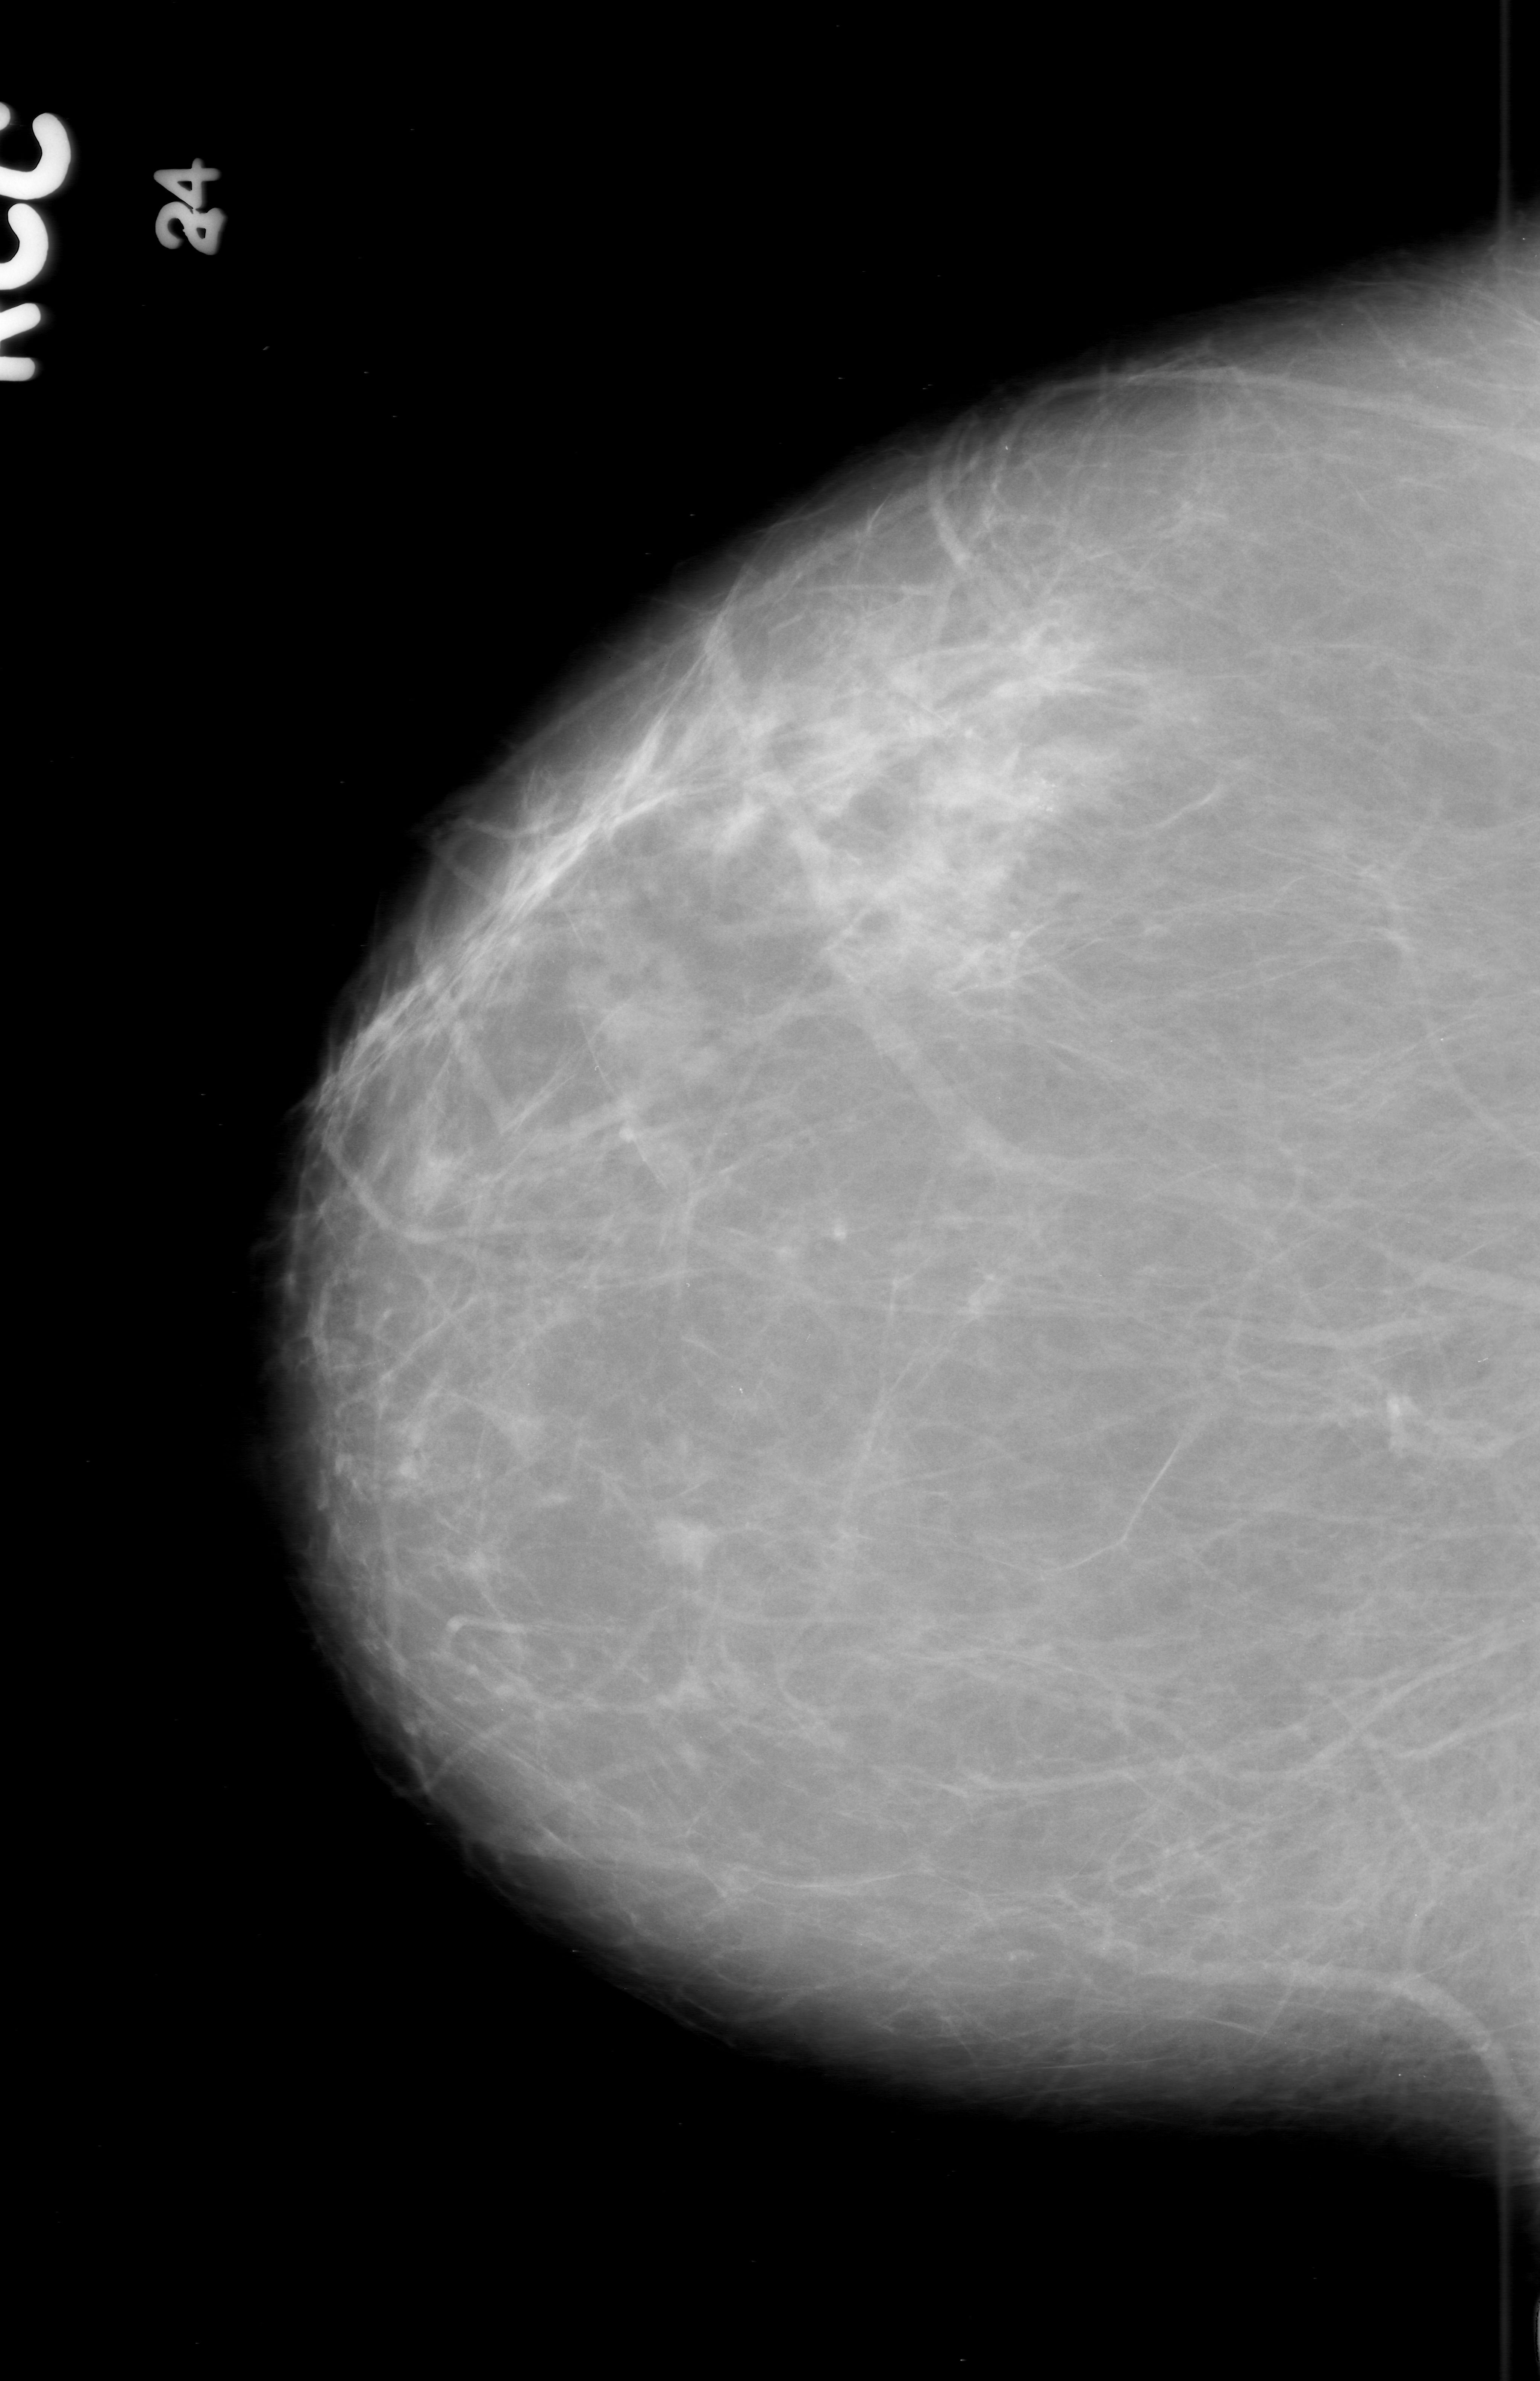
Scanned film-screen mammogram; right breast; CC view; BI-RADS breast density category 2 (scale 1–4).
Marked findings (only marked abnormalities are described; nothing is implied about the rest of the image): calcifications, morphology pleomorphic, distribution clustered; BI-RADS assessment category 0; pathology result (as recorded, not read from the image): benign.